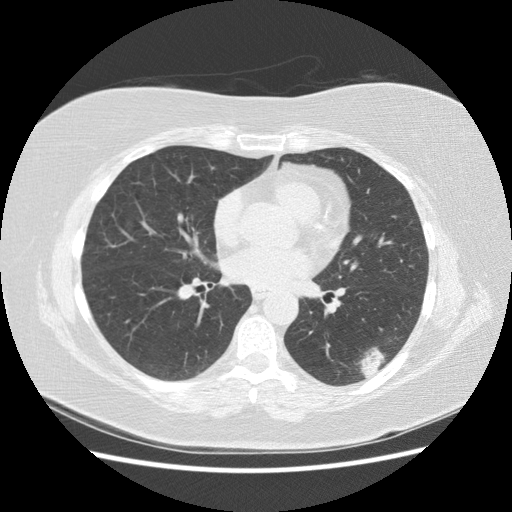
Low-dose screening chest CT, one axial slice. Position 75 of 151 along the scan axis. Reconstruction kernel STANDARD. 120 kVp. Lung window (W 1500 / L -600 HU). 2.5 mm slice thickness. 512 × 512 image matrix, field of view 360 × 360 mm.
Annotated regions visible in this slice (manually delineated by an expert):
- lesion 1 (tumor, lower lobe of left lung): box from (x=359, y=347) to (x=385, y=378) px